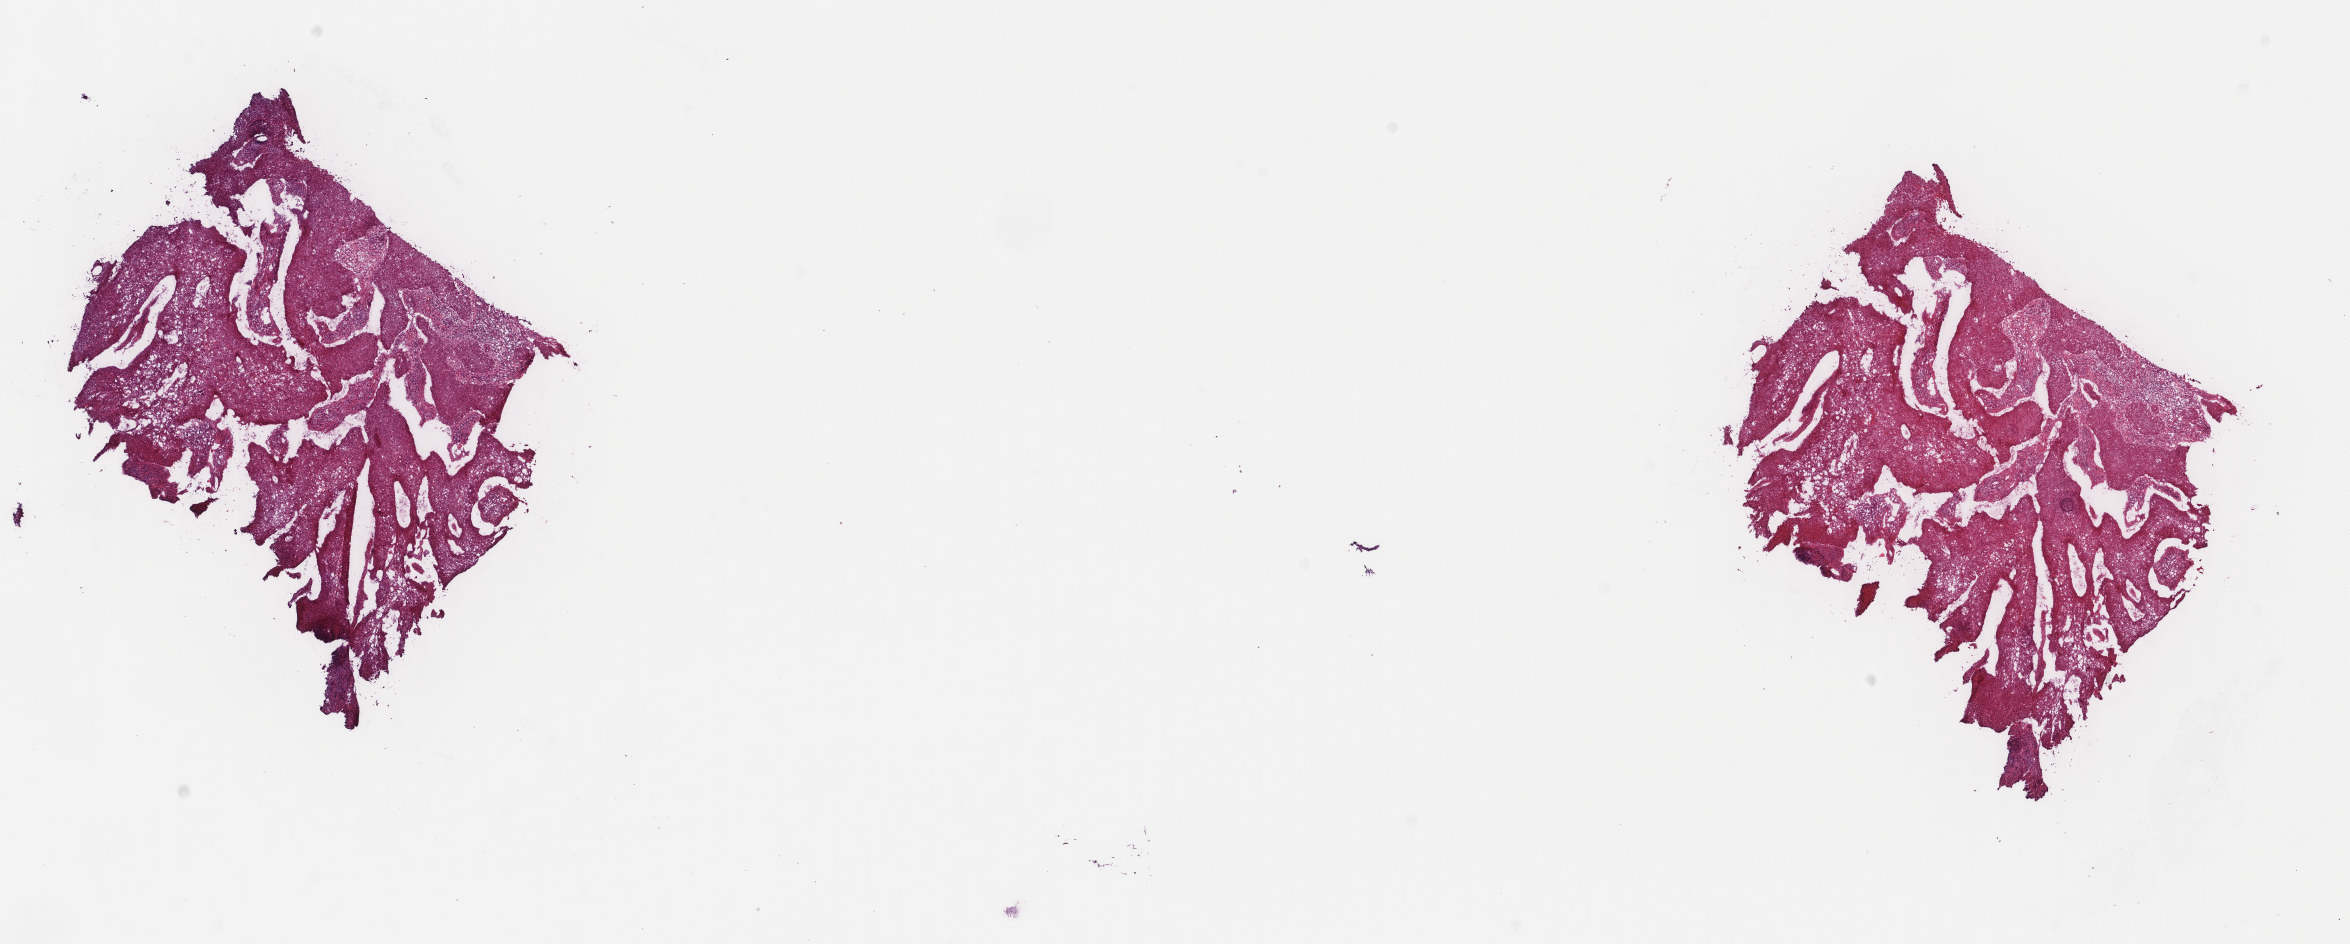
Whole-slide histology image, H&E-stained, shown as a low-resolution overview of the whole scanned area (about 18.7 x 7.5 mm, acquisition: 40x scan); frozen section from the top of the tissue portion; cervix, primary tumour sample. Female patient; age at initial diagnosis 30 years. Slide review estimates, as recorded: tumour cells 80%, tumour nuclei 80%.
Histologic diagnosis: Squamous cell carcinoma, NOS (cervix uteri).